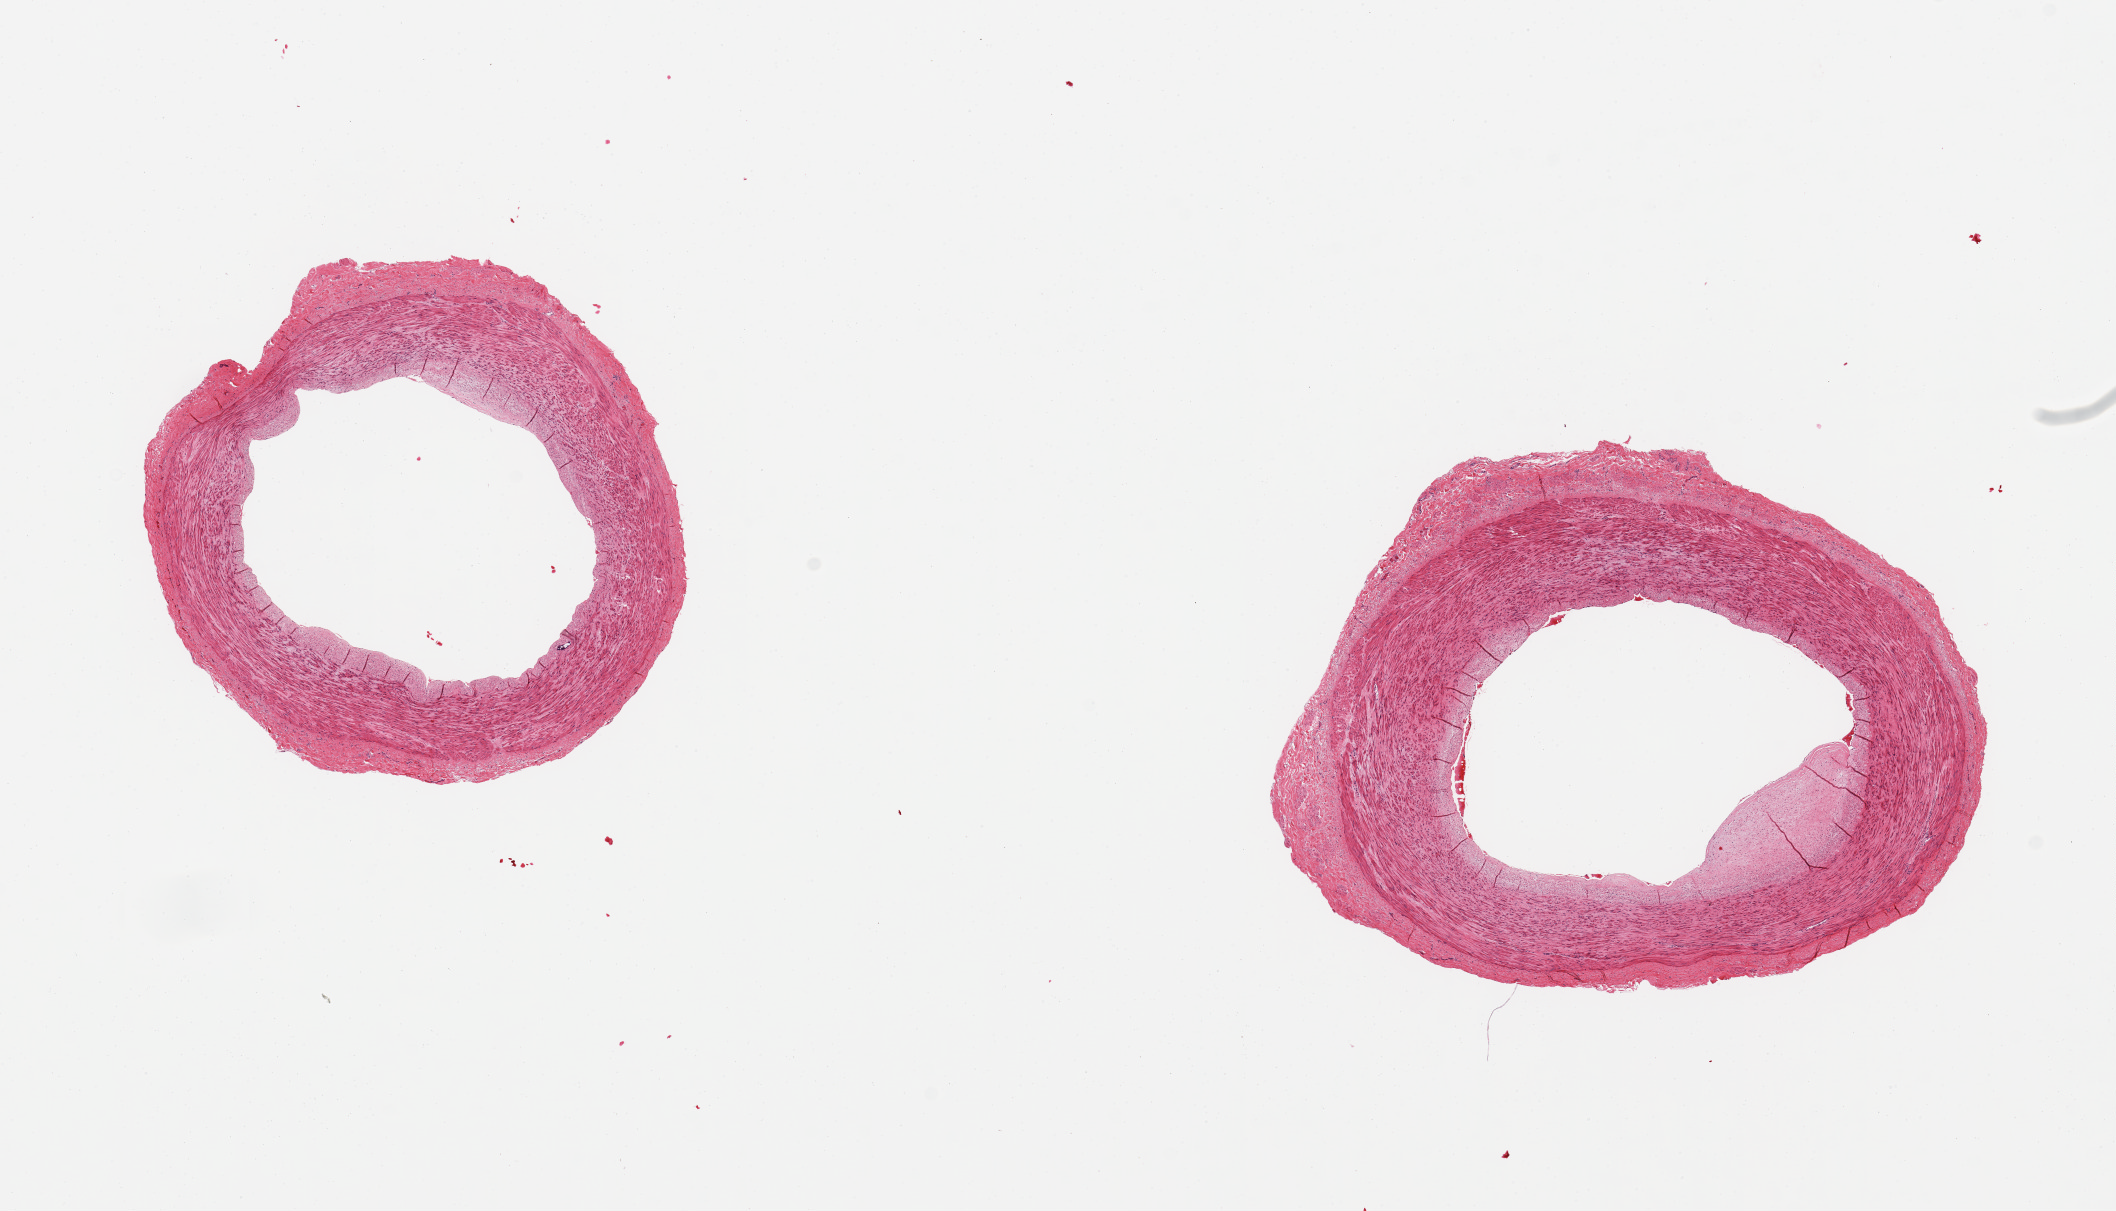
Whole-slide image, haematoxylin and eosin stain, brightfield, whole scanned area (about 16.7 x 9.6 mm) shown as a low-resolution overview; PAXgene-fixed, paraffin-embedded tissue; sampled site (target tissue): tibial artery; donor tissue sample. Donor: male.
Reviewer comment on this tissue sample: 2 pieces, excellent clean specimens; ~10% luminal atherotic occlusion in one section.